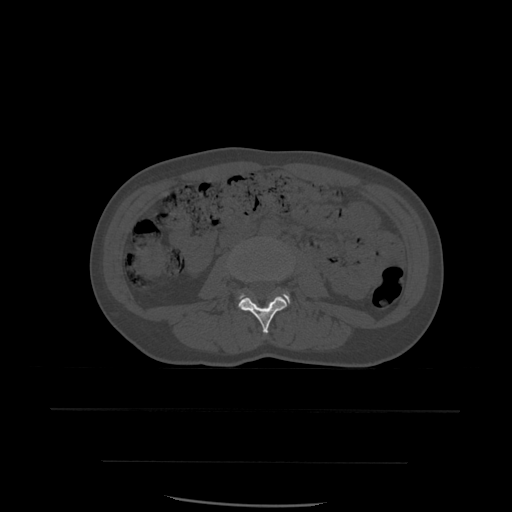
CT including the spine, one axial slice. Bone window (W 1800 / L 400 HU). 1.25 mm slice thickness. 512 × 512 image matrix, field of view 392 × 392 mm. Patient age 48 years. Case-level facts recorded for this patient, not image findings: primary cancer: lung; vertebrae with lytic lesions (as recorded): T11.
Outlined on this slice (semi-automatically segmented with operator editing):
- L3 vertebra: bounding box [x1, y1, x2, y2] px = [230, 267, 287, 334]
- L4 vertebra: [241, 293, 291, 304]